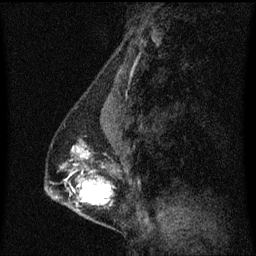
Breast MRI (dynamic contrast-enhanced), one sagittal slice; position 25 of 60 along the scan axis; dynamic contrast-enhanced series, image 2 of 3 at this slice position (ordered by acquisition); 1.5 T; TE 4.2 ms, TR 8.4 ms; 2 mm slice thickness; 256 × 256 image matrix, field of view 200 × 200 mm. Patient: female, 40 years. From the clinical record (not read from this slice): setting: breast cancer imaged before/during neoadjuvant chemotherapy; receptor status: triple-negative.
Structures marked on this image (semi-automatic segmentation, software-assisted and operator-edited):
- analysis volume of interest (the breast-tissue region the enhancement analysis was run in; not a lesion): bounding box (x1, y1, x2, y2) in pixels: (47, 128, 120, 221)
- tumour enhancement mask (voxels above the 70 % enhancement threshold inside the analysis volume of interest): (79, 150, 112, 205)